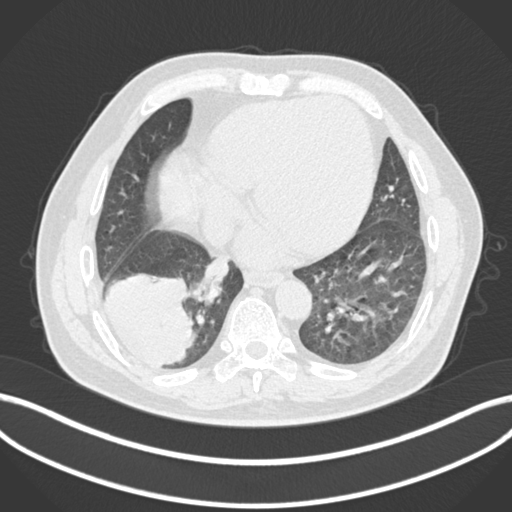
Chest CT, one axial slice. Position 47 of 200 along the scan axis. Reconstruction kernel B30f. Lung window (W 1500 / L -600 HU). 512 × 512 image matrix, field of view 400 × 400 mm. Patient: male, 59 years.
Structures marked on this image (rectangle marked by the reading radiologist):
- lung tumour (recorded histology: adenocarcinoma): bounding box [x1, y1, x2, y2] px = [100, 268, 200, 374]